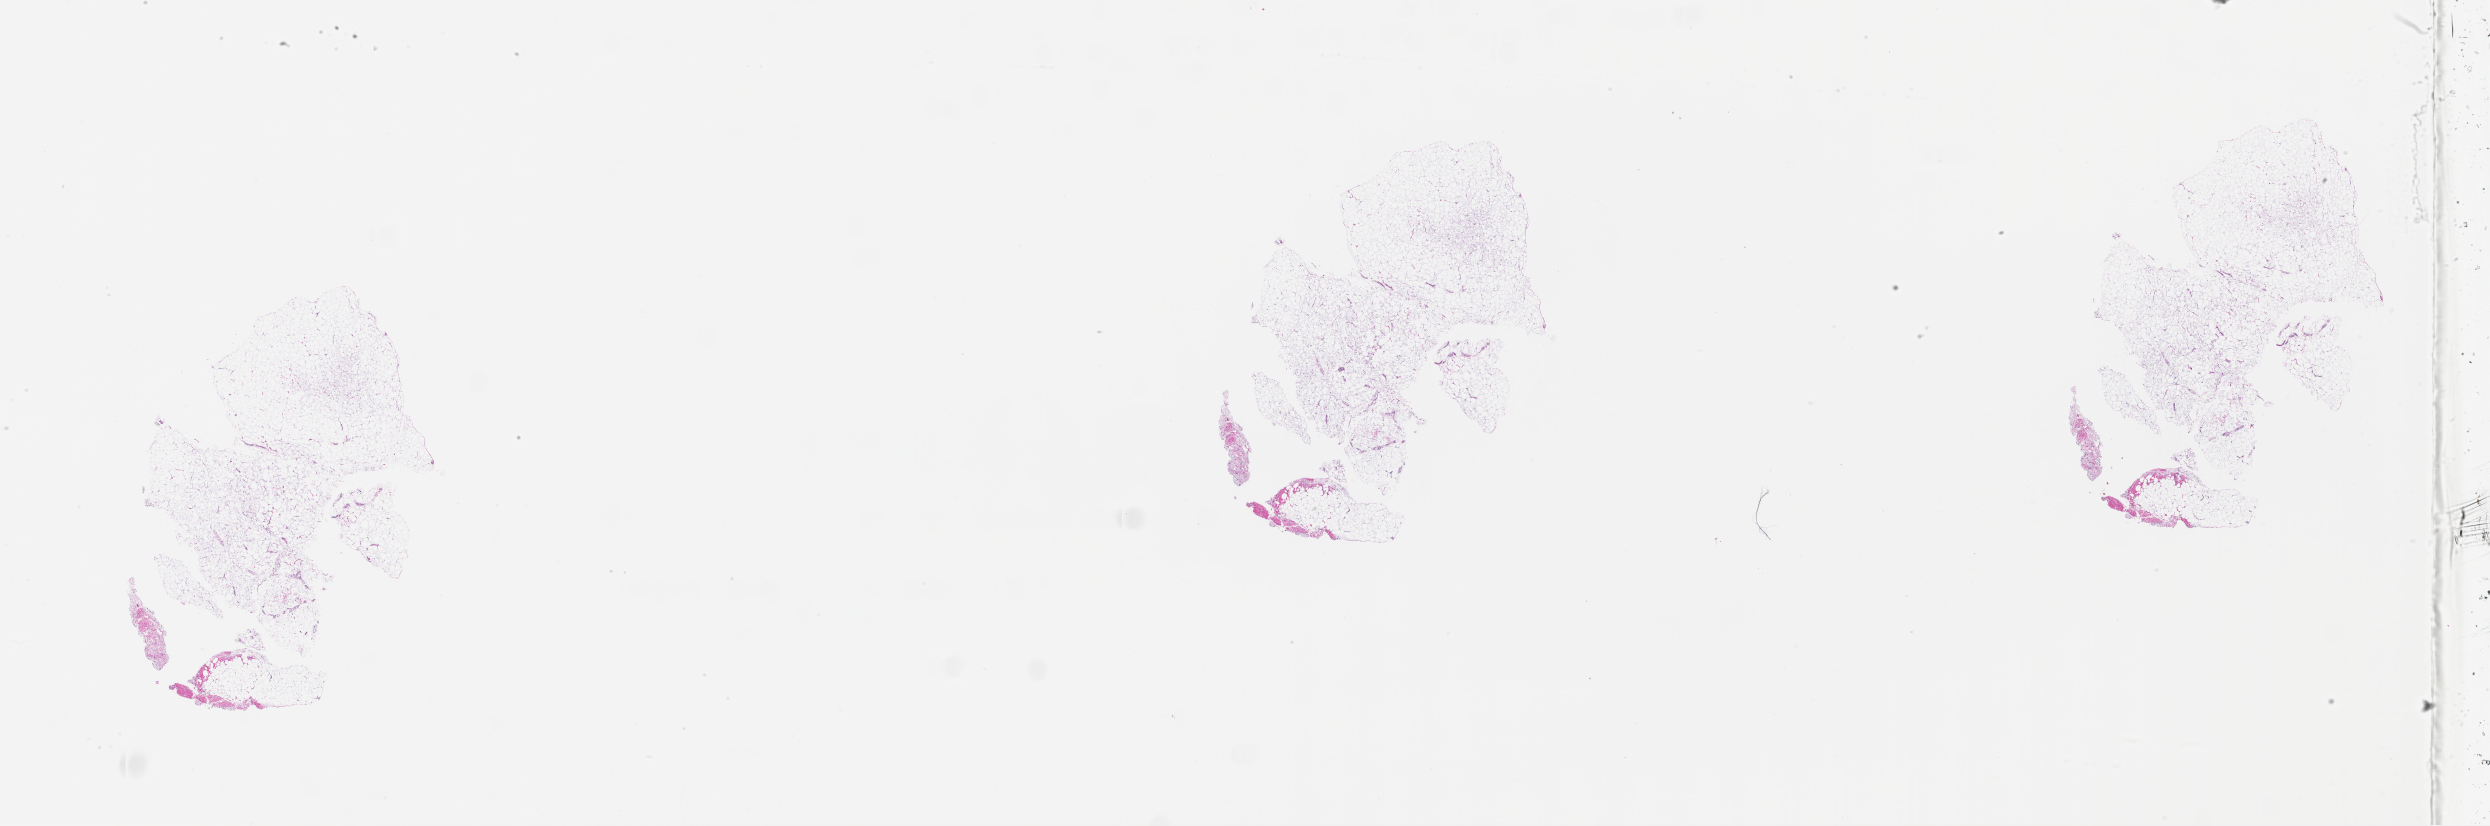
Whole-slide histology image, H&E — whole scanned area (about 40.1 x 13.3 mm, slide scanned at 20x) shown as a low-resolution overview.
Patient diagnosis (cohort enrolment): sarcoma (site not recorded at cohort level).